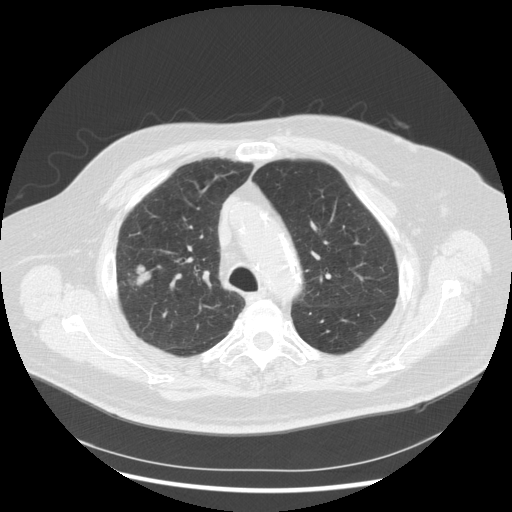
Low-dose screening chest CT, one axial slice. Position 206 of 263 along the scan axis. Reconstruction kernel STANDARD. Lung window (W 1500 / L -600 HU). 2.5 mm slice thickness. 512 × 512 image matrix, field of view 400 × 400 mm.
Outlined on this slice (outlined manually by an expert reader):
- lesion 1 (tumor, upper lobe of right lung): box from (x=137, y=266) to (x=150, y=284) px